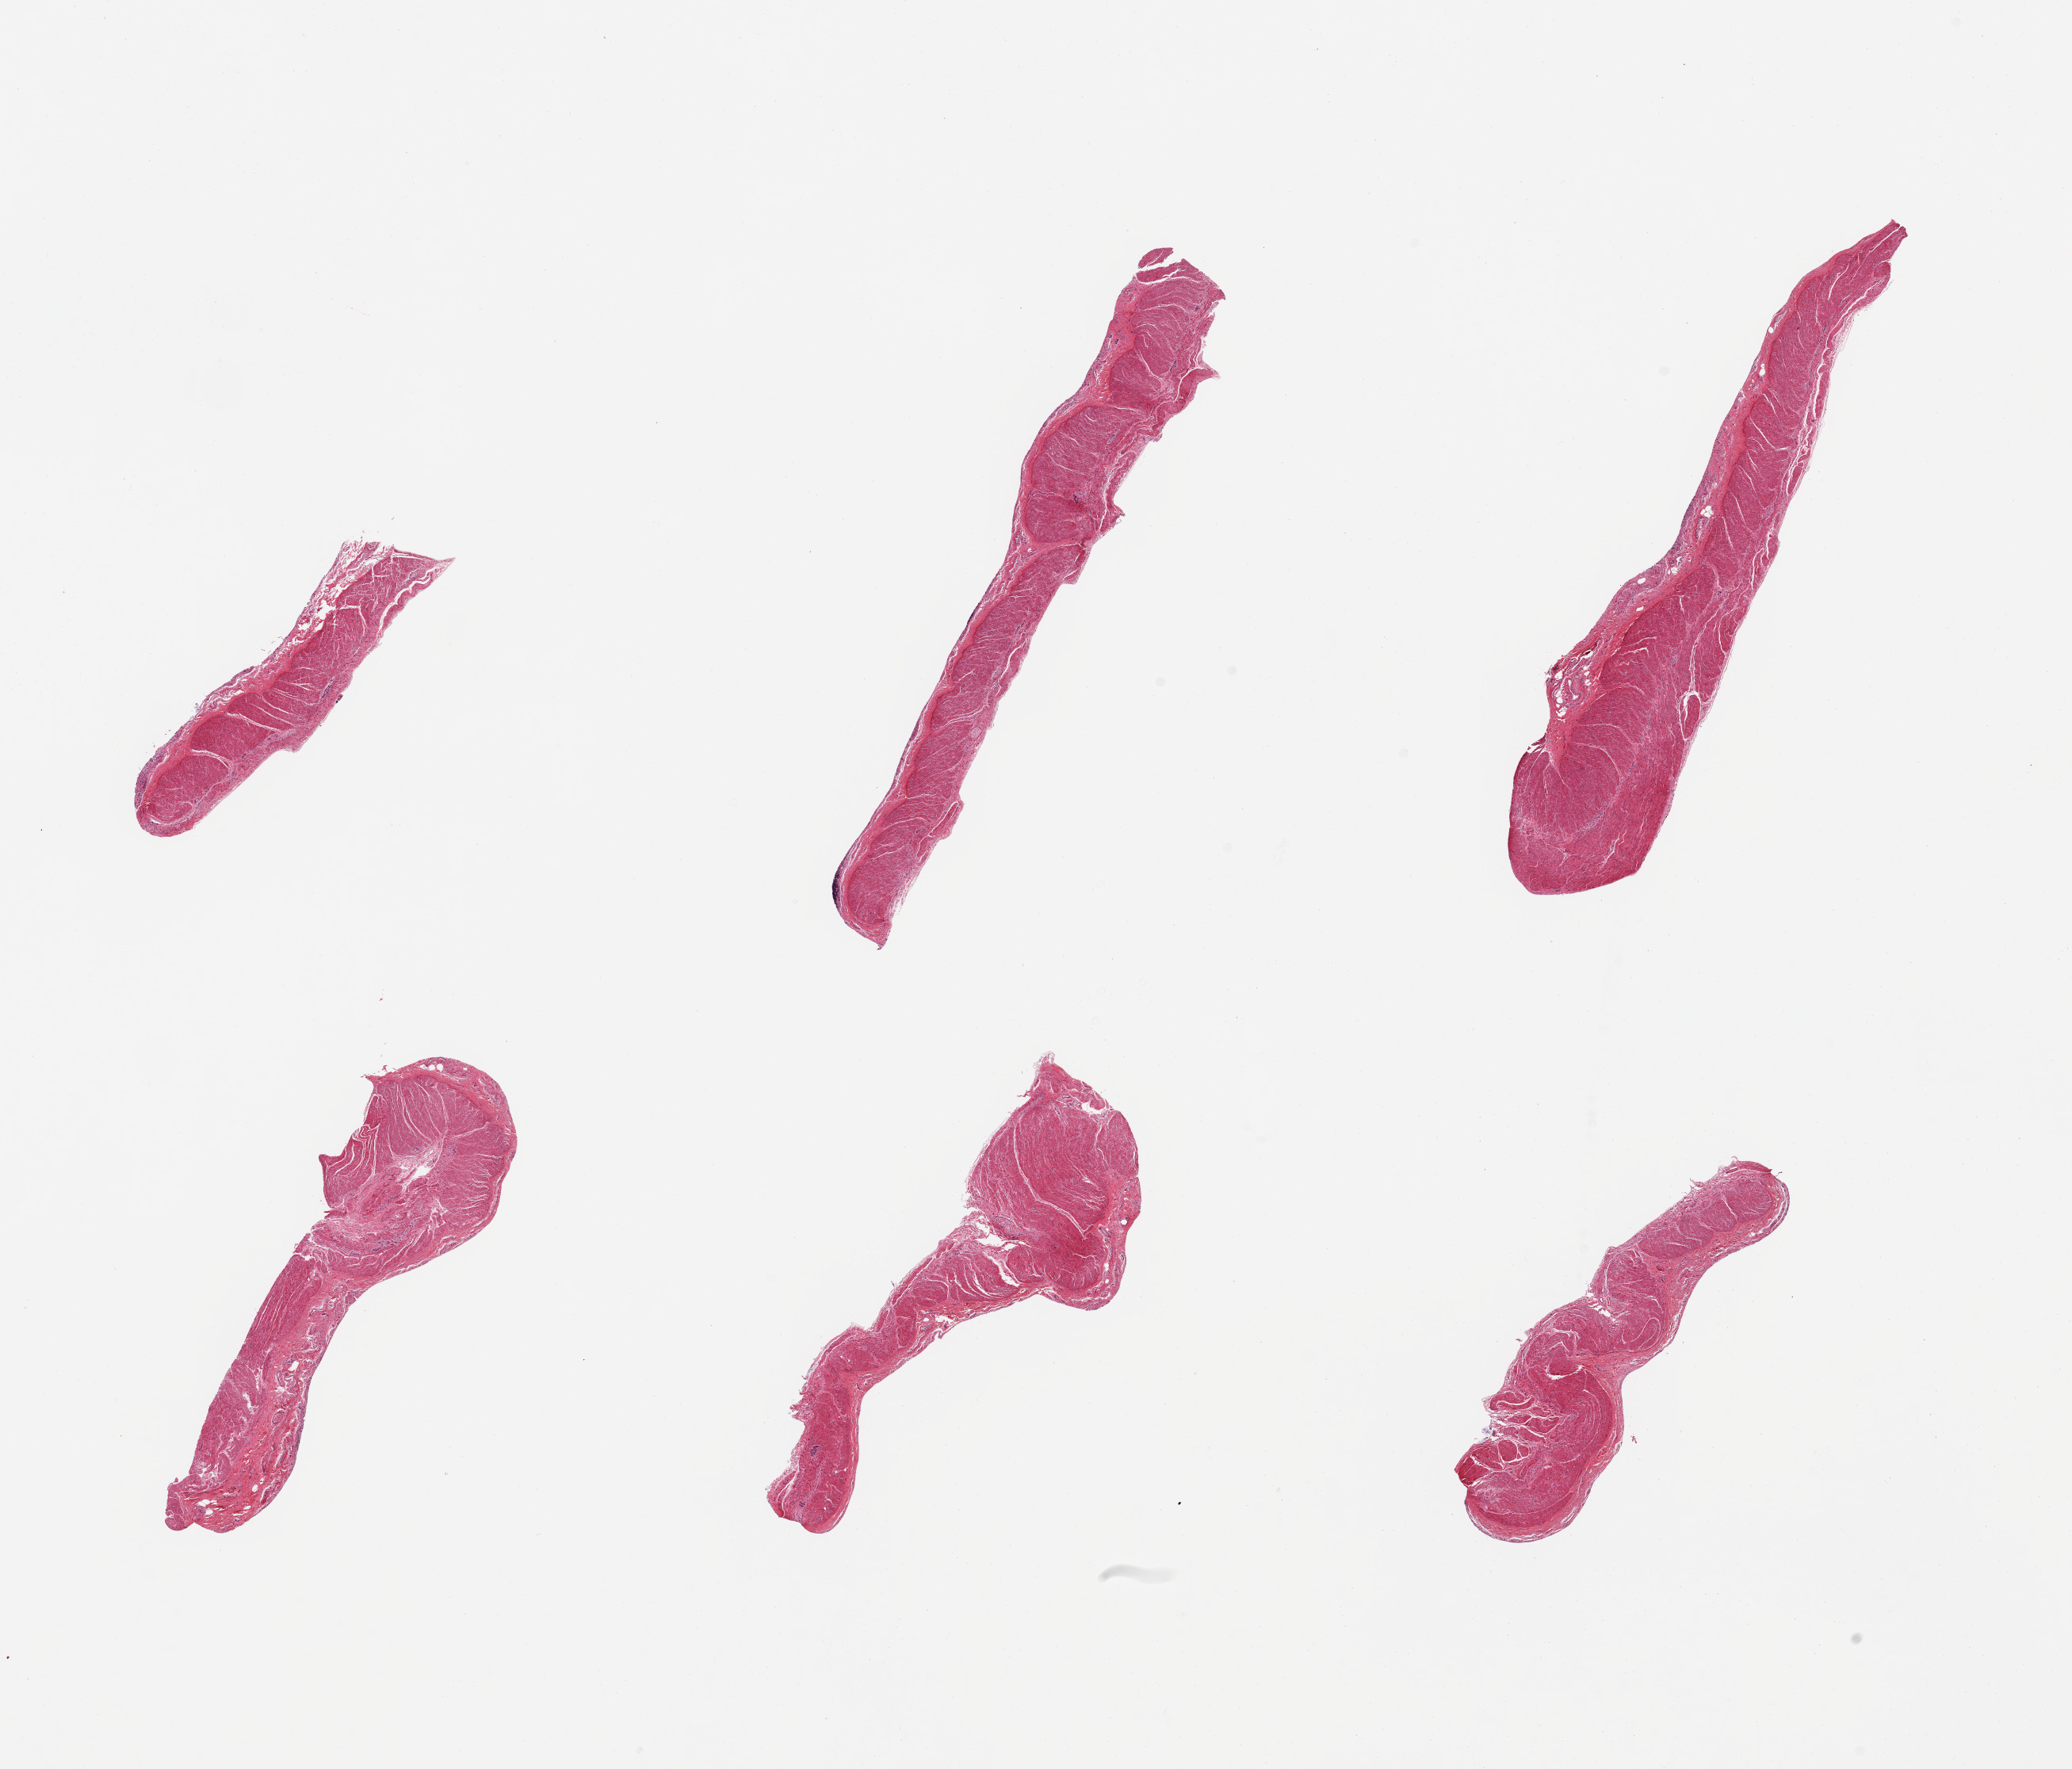
Whole-slide image, H&E stain, brightfield, shown as a low-resolution overview of the whole scanned area (about 20.7 x 17.7 mm, from a 20x scan). PAXgene-fixed paraffin-embedded (PFPE) section. Target tissue: sigmoid colon. Tissue donor sample. Donor: male.
Reviewer comment on this tissue sample: 6 pieces; well dissected muscularis.